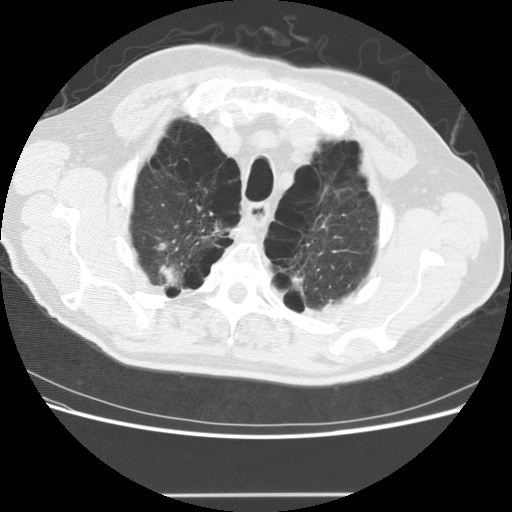
Chest CT (low-dose screening protocol), one axial image, third annual screen, lung window (W 1500 / L -600 HU), 2.5 mm slice thickness, standard (soft-tissue) reconstruction kernel (STANDARD), 120 kVp, slice 31 of 151 in the series, 512 × 512 image matrix, field of view 360 × 360 mm. Male participant, aged 68 years at enrolment. Former smoker at enrolment.
• Lesion marked by an expert reader, bounding box <128,217,214,298> (left, top, right, bottom; pixels).
• The screening reader recorded 2 non-calcified nodules or masses ≥4 mm on this exam (lingula, left lower lobe); which of them this box marks is not recorded.
• Official screen result: positive, no significant change: stable abnormalities potentially related to lung cancer, unchanged since the prior screening exam.